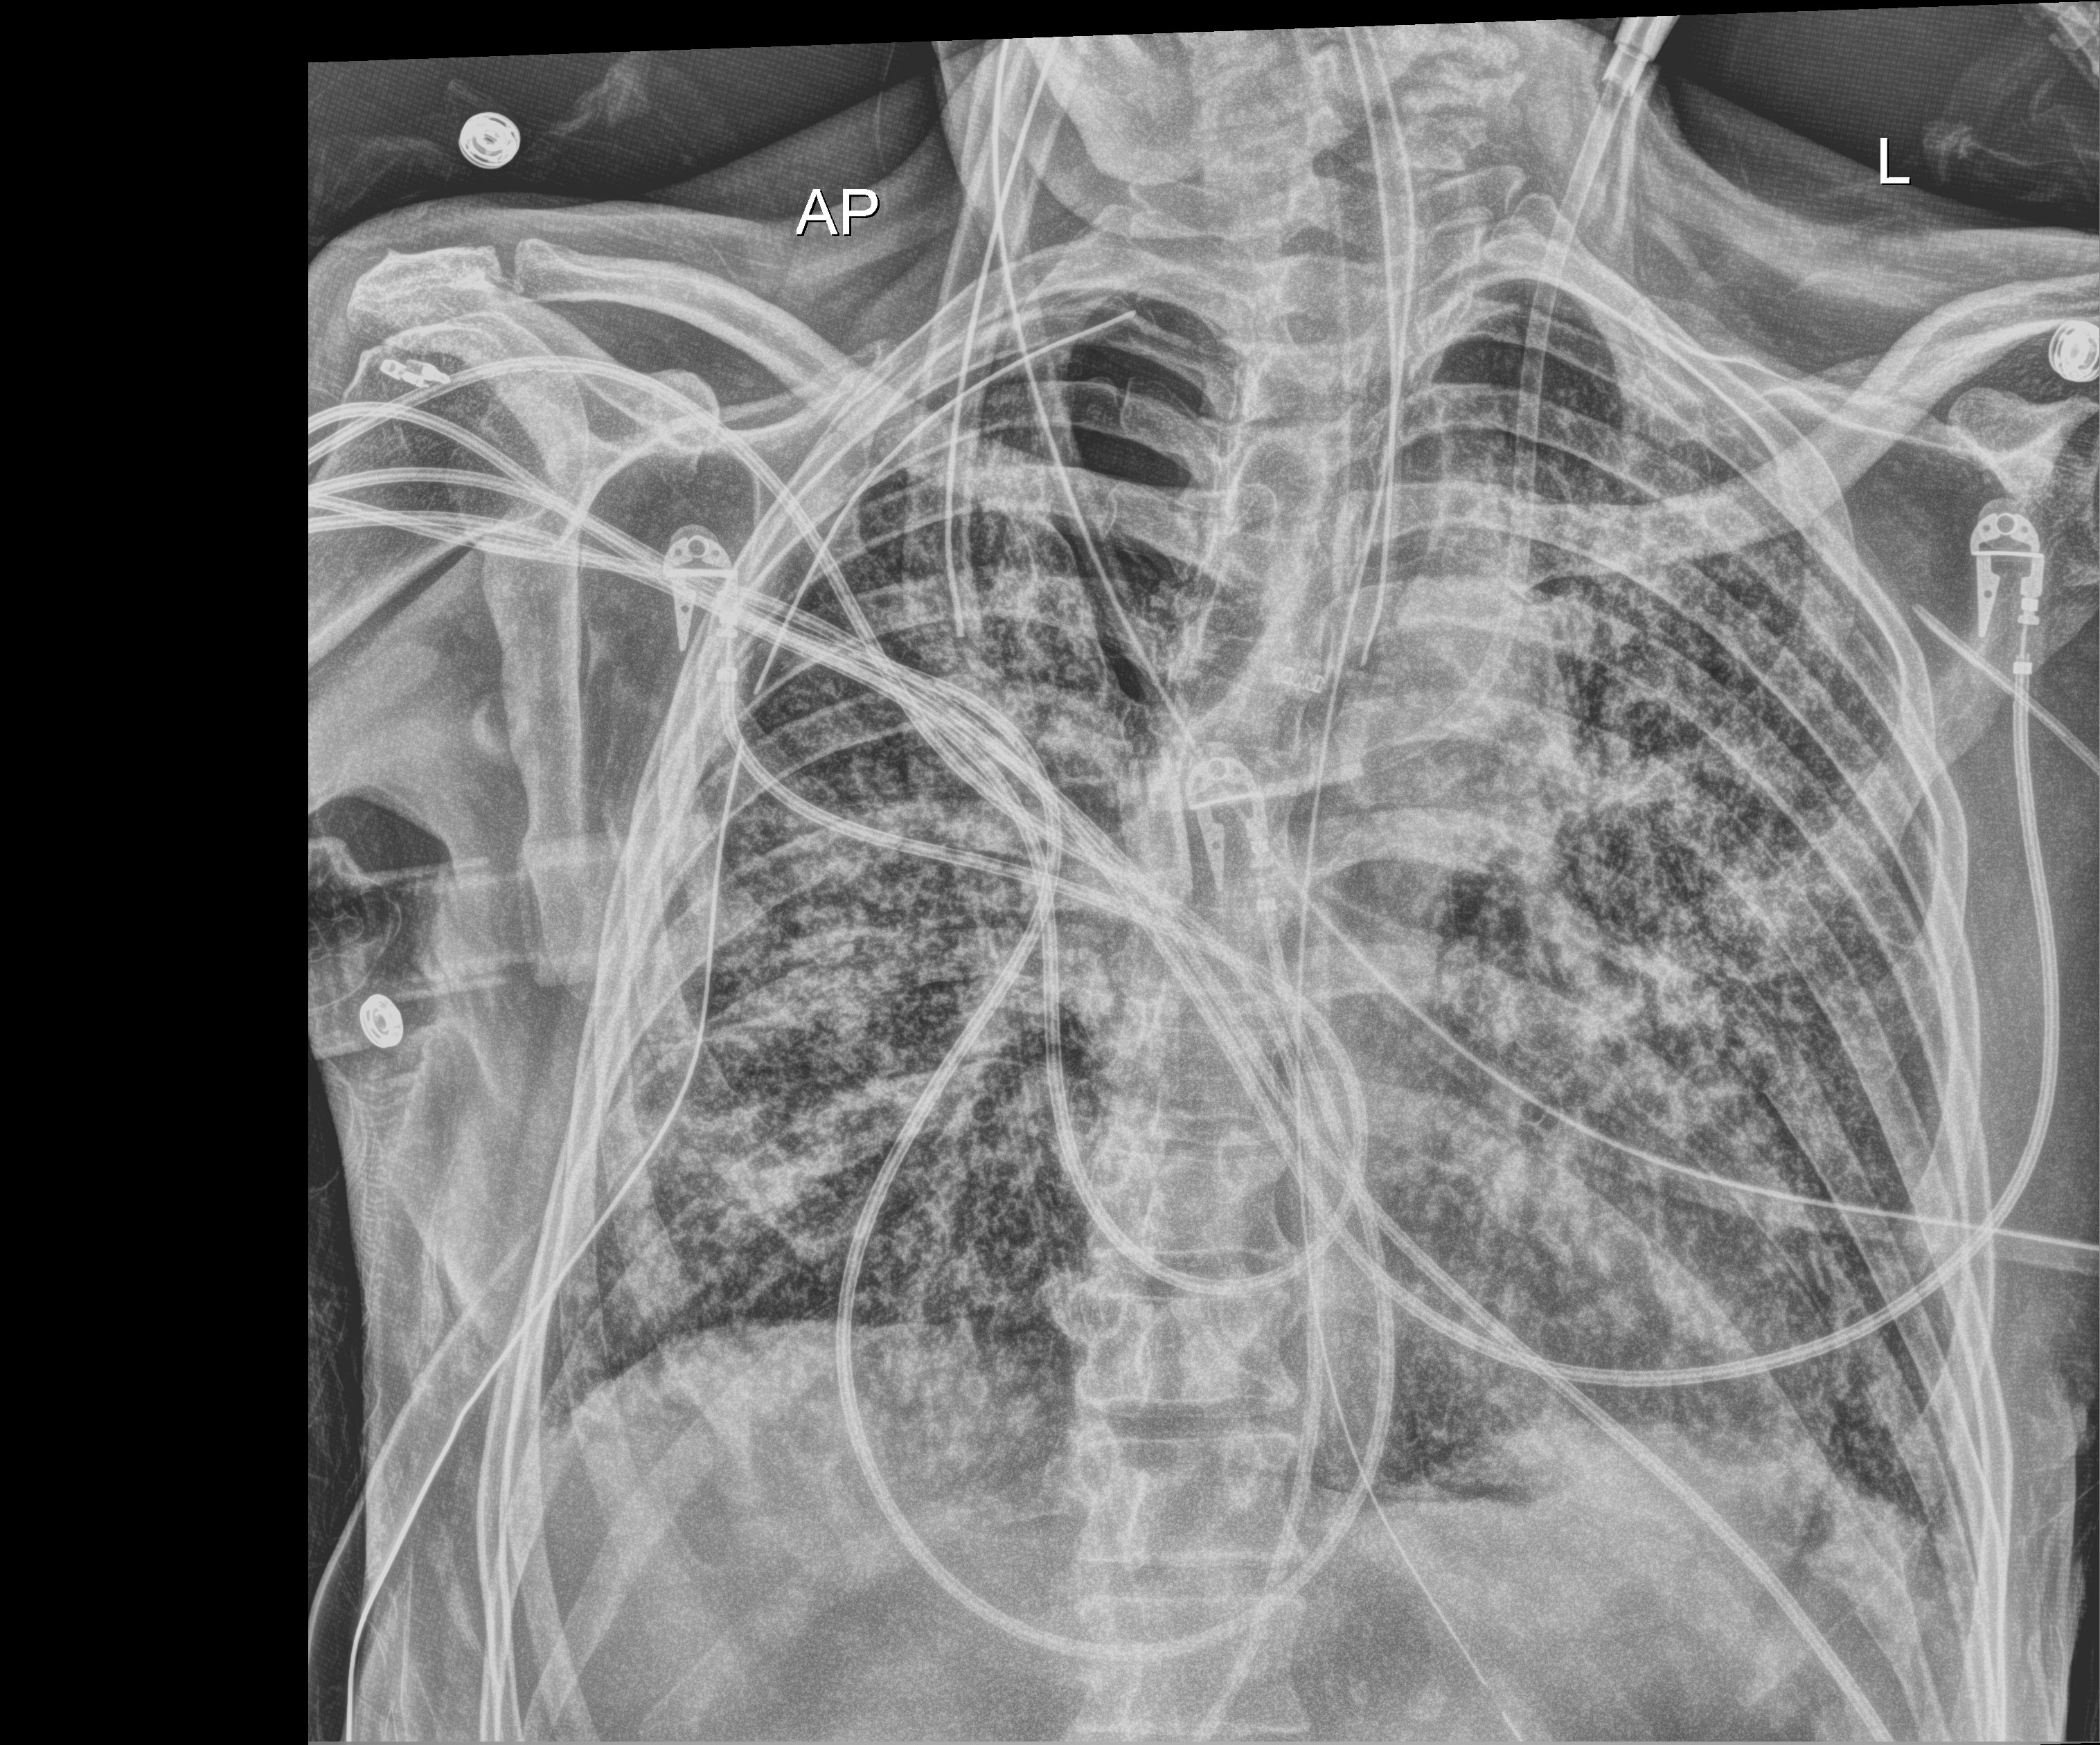
Chest X-ray (portable); anteroposterior (AP) projection. Male patient hospitalised with COVID-19, age 60–74 years.
Admission-level facts for this patient (not findings on this image; timing relative to this image not recorded): mechanically ventilated during this hospital stay: yes; other chronic lung disease (admission record): yes; admitted to intensive care during this hospital stay: yes.